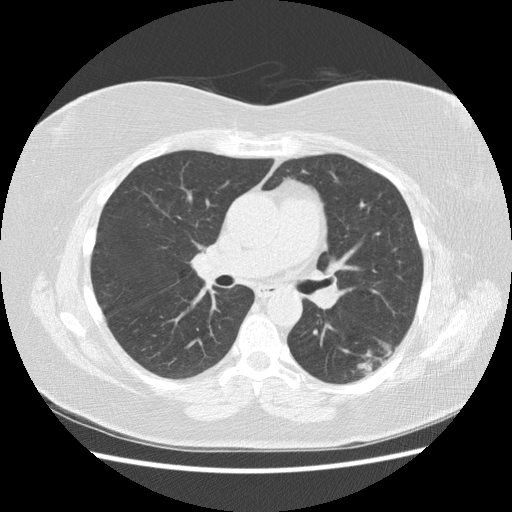
Low-dose screening chest CT, one axial slice; slice 88 of 151 in the series (ordered by position); 120 kVp; lung window (W 1500 / L -600 HU); 2.5 mm slice thickness; 512 × 512 image matrix, field of view 360 × 360 mm.
Annotated regions visible in this slice (outlined manually by an expert reader):
- lesion 1 (tumor, lower lobe of left lung): box from (x=356, y=341) to (x=397, y=372) px